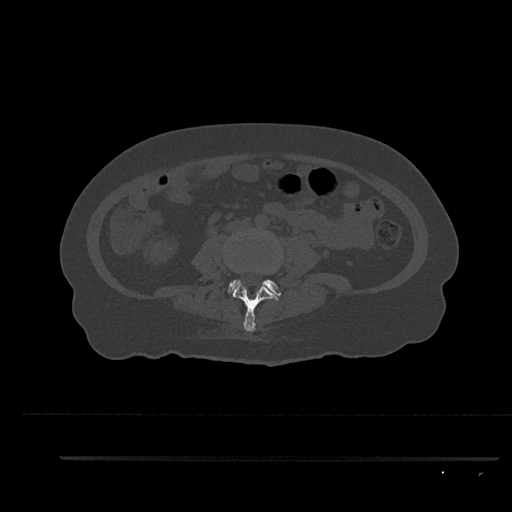
CT including the spine, one axial slice. Slice 57 of 797 in the series (ordered by position). Bone window (W 1800 / L 400 HU). 0.5 mm slice thickness. 512 × 512 image matrix, field of view 408 × 408 mm. Female patient, age 44 years. From the clinical record (not read from this slice): primary cancer: renal; vertebrae with lytic lesions (as recorded): L1.
Outlined on this slice (semi-automatically segmented with operator editing):
- L3 vertebra: box from (x=232, y=282) to (x=280, y=332) px
- L4 vertebra: (x=227, y=279)–(x=282, y=296)